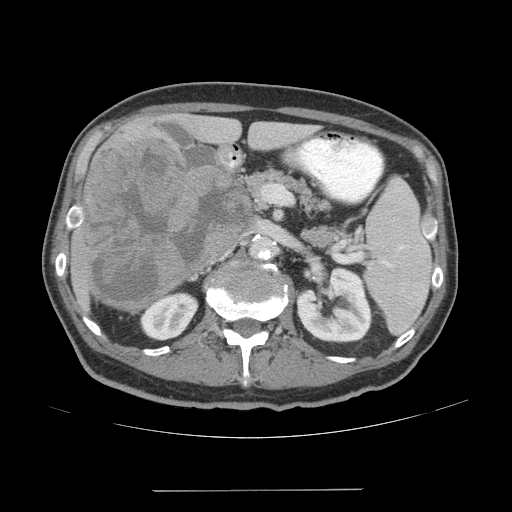
Contrast-enhanced abdominal CT (liver protocol), one axial slice. Position 23 of 77 along the scan axis. Reconstruction kernel STANDARD. 140 kVp. Soft-tissue window (W 400 / L 40 HU). 2.5 mm slice thickness. 512 × 512 image matrix. Case-level facts recorded for this patient, not image findings: diagnosis: hepatocellular carcinoma (patient treated with transarterial chemoembolisation; whether this scan precedes or follows treatment is not stated here); TNM stage (as recorded): Stage-IVA; Child-Pugh class: A; tumour nodularity: uninodular.
Structures marked on this image (semi-automatically segmented with operator editing):
- liver parenchyma outside the tumour (the mass and vessels are separate outlines, so this box may not span the whole liver): bounding box (x1, y1, x2, y2) in pixels: (70, 116, 313, 313)
- mass: (82, 139, 252, 311)